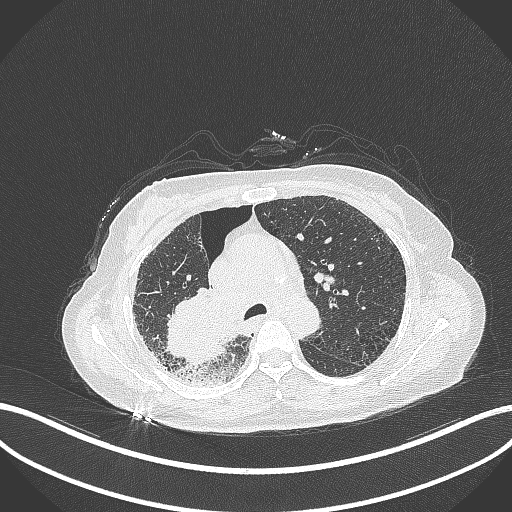
Chest CT, one axial slice. Position 231 of 408 along the scan axis. Reconstruction kernel B70f. 120 kVp. Lung window (W 1500 / L -600 HU). 1 mm slice thickness. 512 × 512 image matrix, field of view 400 × 400 mm. Patient: female, 64 years. From the clinical record (not read from this slice): clinical TNM (as recorded): T3 N3 M0.
Annotated regions visible in this slice (bounding box drawn by a radiologist):
- lung tumour (recorded histology: squamous cell carcinoma): bounding box [x1, y1, x2, y2] px = [162, 282, 234, 371]